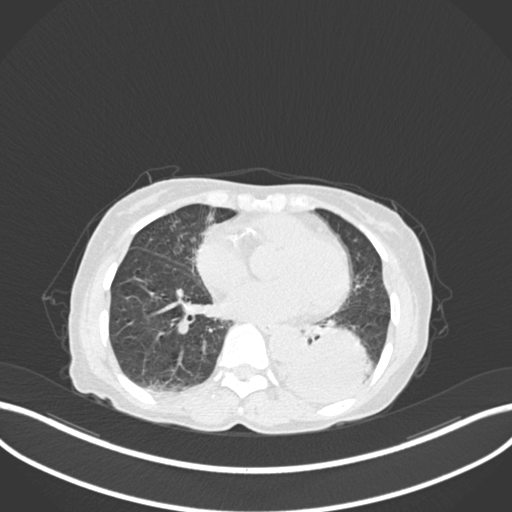
Chest CT, one axial slice; position 51 of 233 along the scan axis; reconstruction kernel B30f; 120 kVp; lung window (W 1500 / L -600 HU); 1 mm slice thickness; 512 × 512 image matrix, field of view 400 × 400 mm. Patient: female, 78 years. Case-level facts recorded for this patient, not image findings: clinical TNM (as recorded): T3 N0 M1.
Structures marked on this image (bounding box drawn by a radiologist):
- lung tumour (recorded histology: squamous cell carcinoma): bounding box (x1, y1, x2, y2) in pixels: (280, 314, 373, 400)